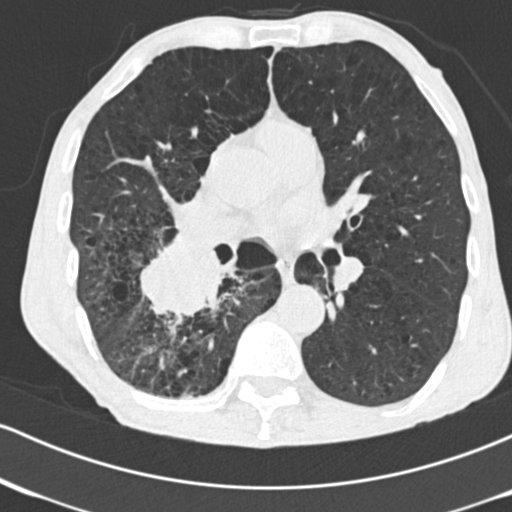
Low-dose screening chest CT, one axial slice. Slice 88 of 182 in the series (ordered by position). Reconstruction kernel B30f. Lung window (W 1500 / L -600 HU). 2 mm slice thickness. 512 × 512 image matrix, field of view 316 × 316 mm.
Annotated regions visible in this slice (expert manual segmentation):
- lesion 1 (tumor, lower lobe of right lung): bounding box <140,237,226,318> (left, top, right, bottom; pixels)